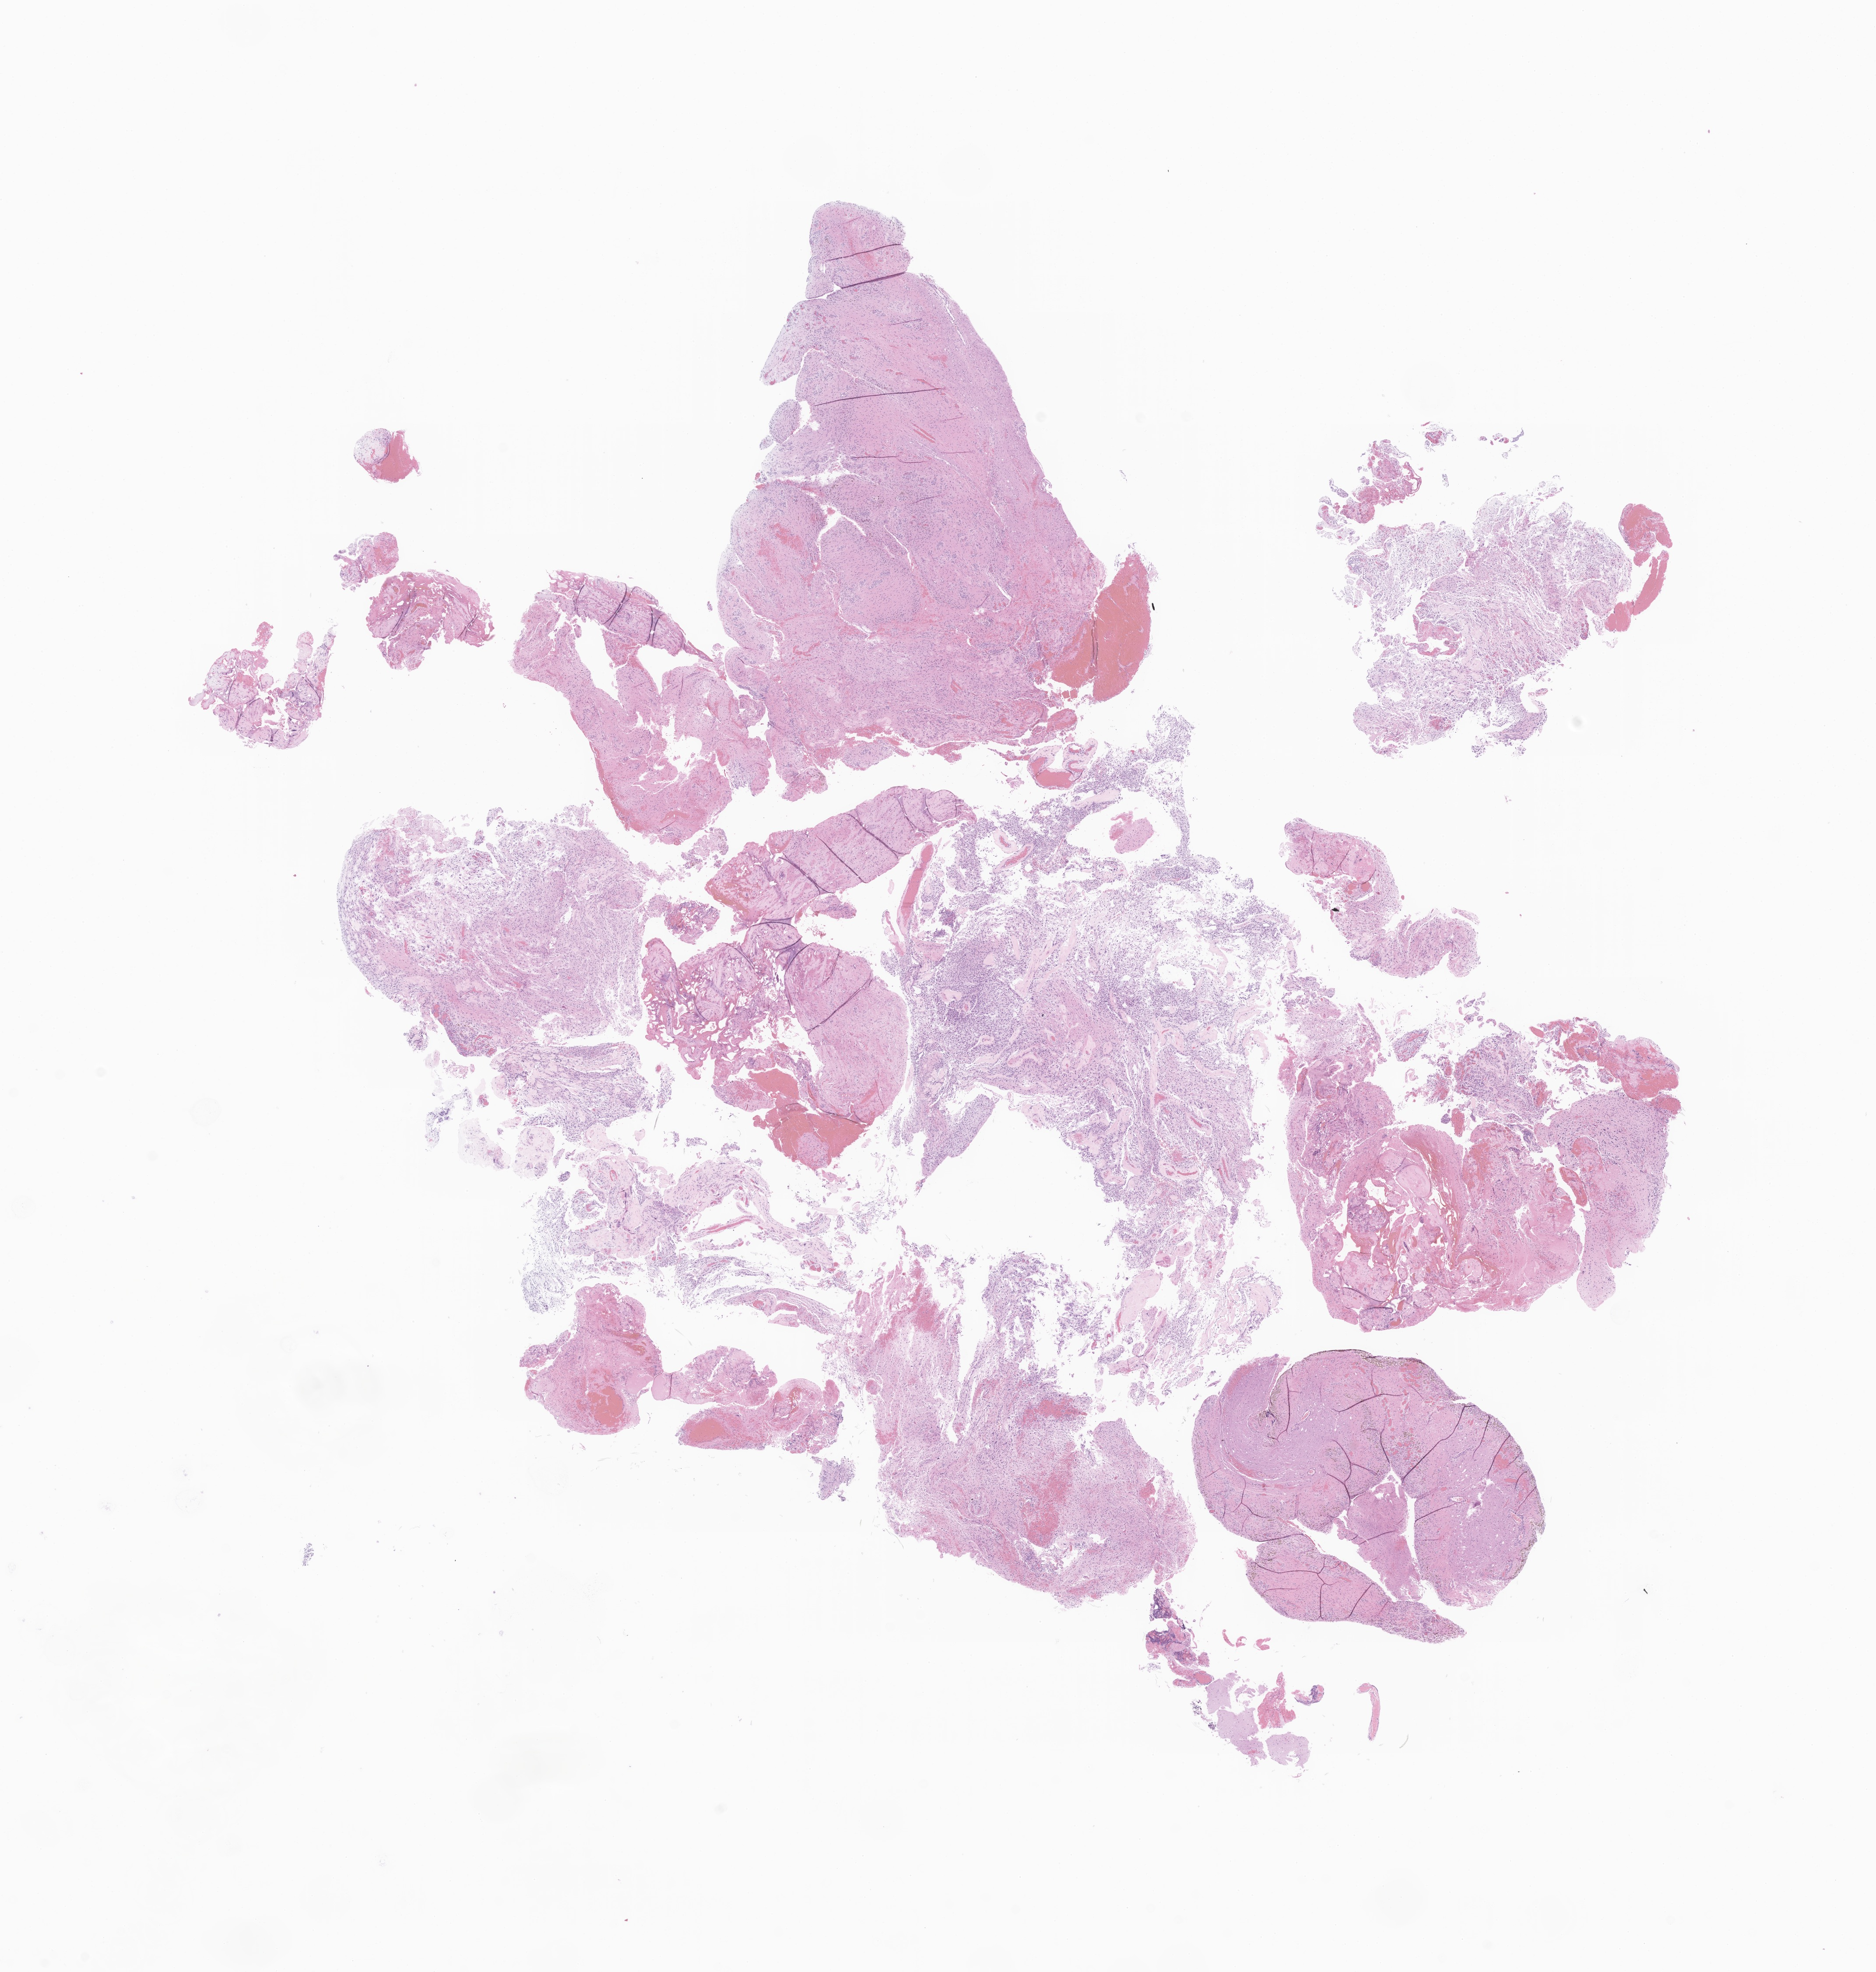
Digitized hematoxylin and eosin (H&E)-stained section of tumor tissue from the cerebral ventricle, low-resolution overview of the scanned area, about 18.1 x 19.0 mm, FFPE section. Patient male; age 137 months (11 years 5 months).
Diagnosis: Pilocytic astrocytoma.